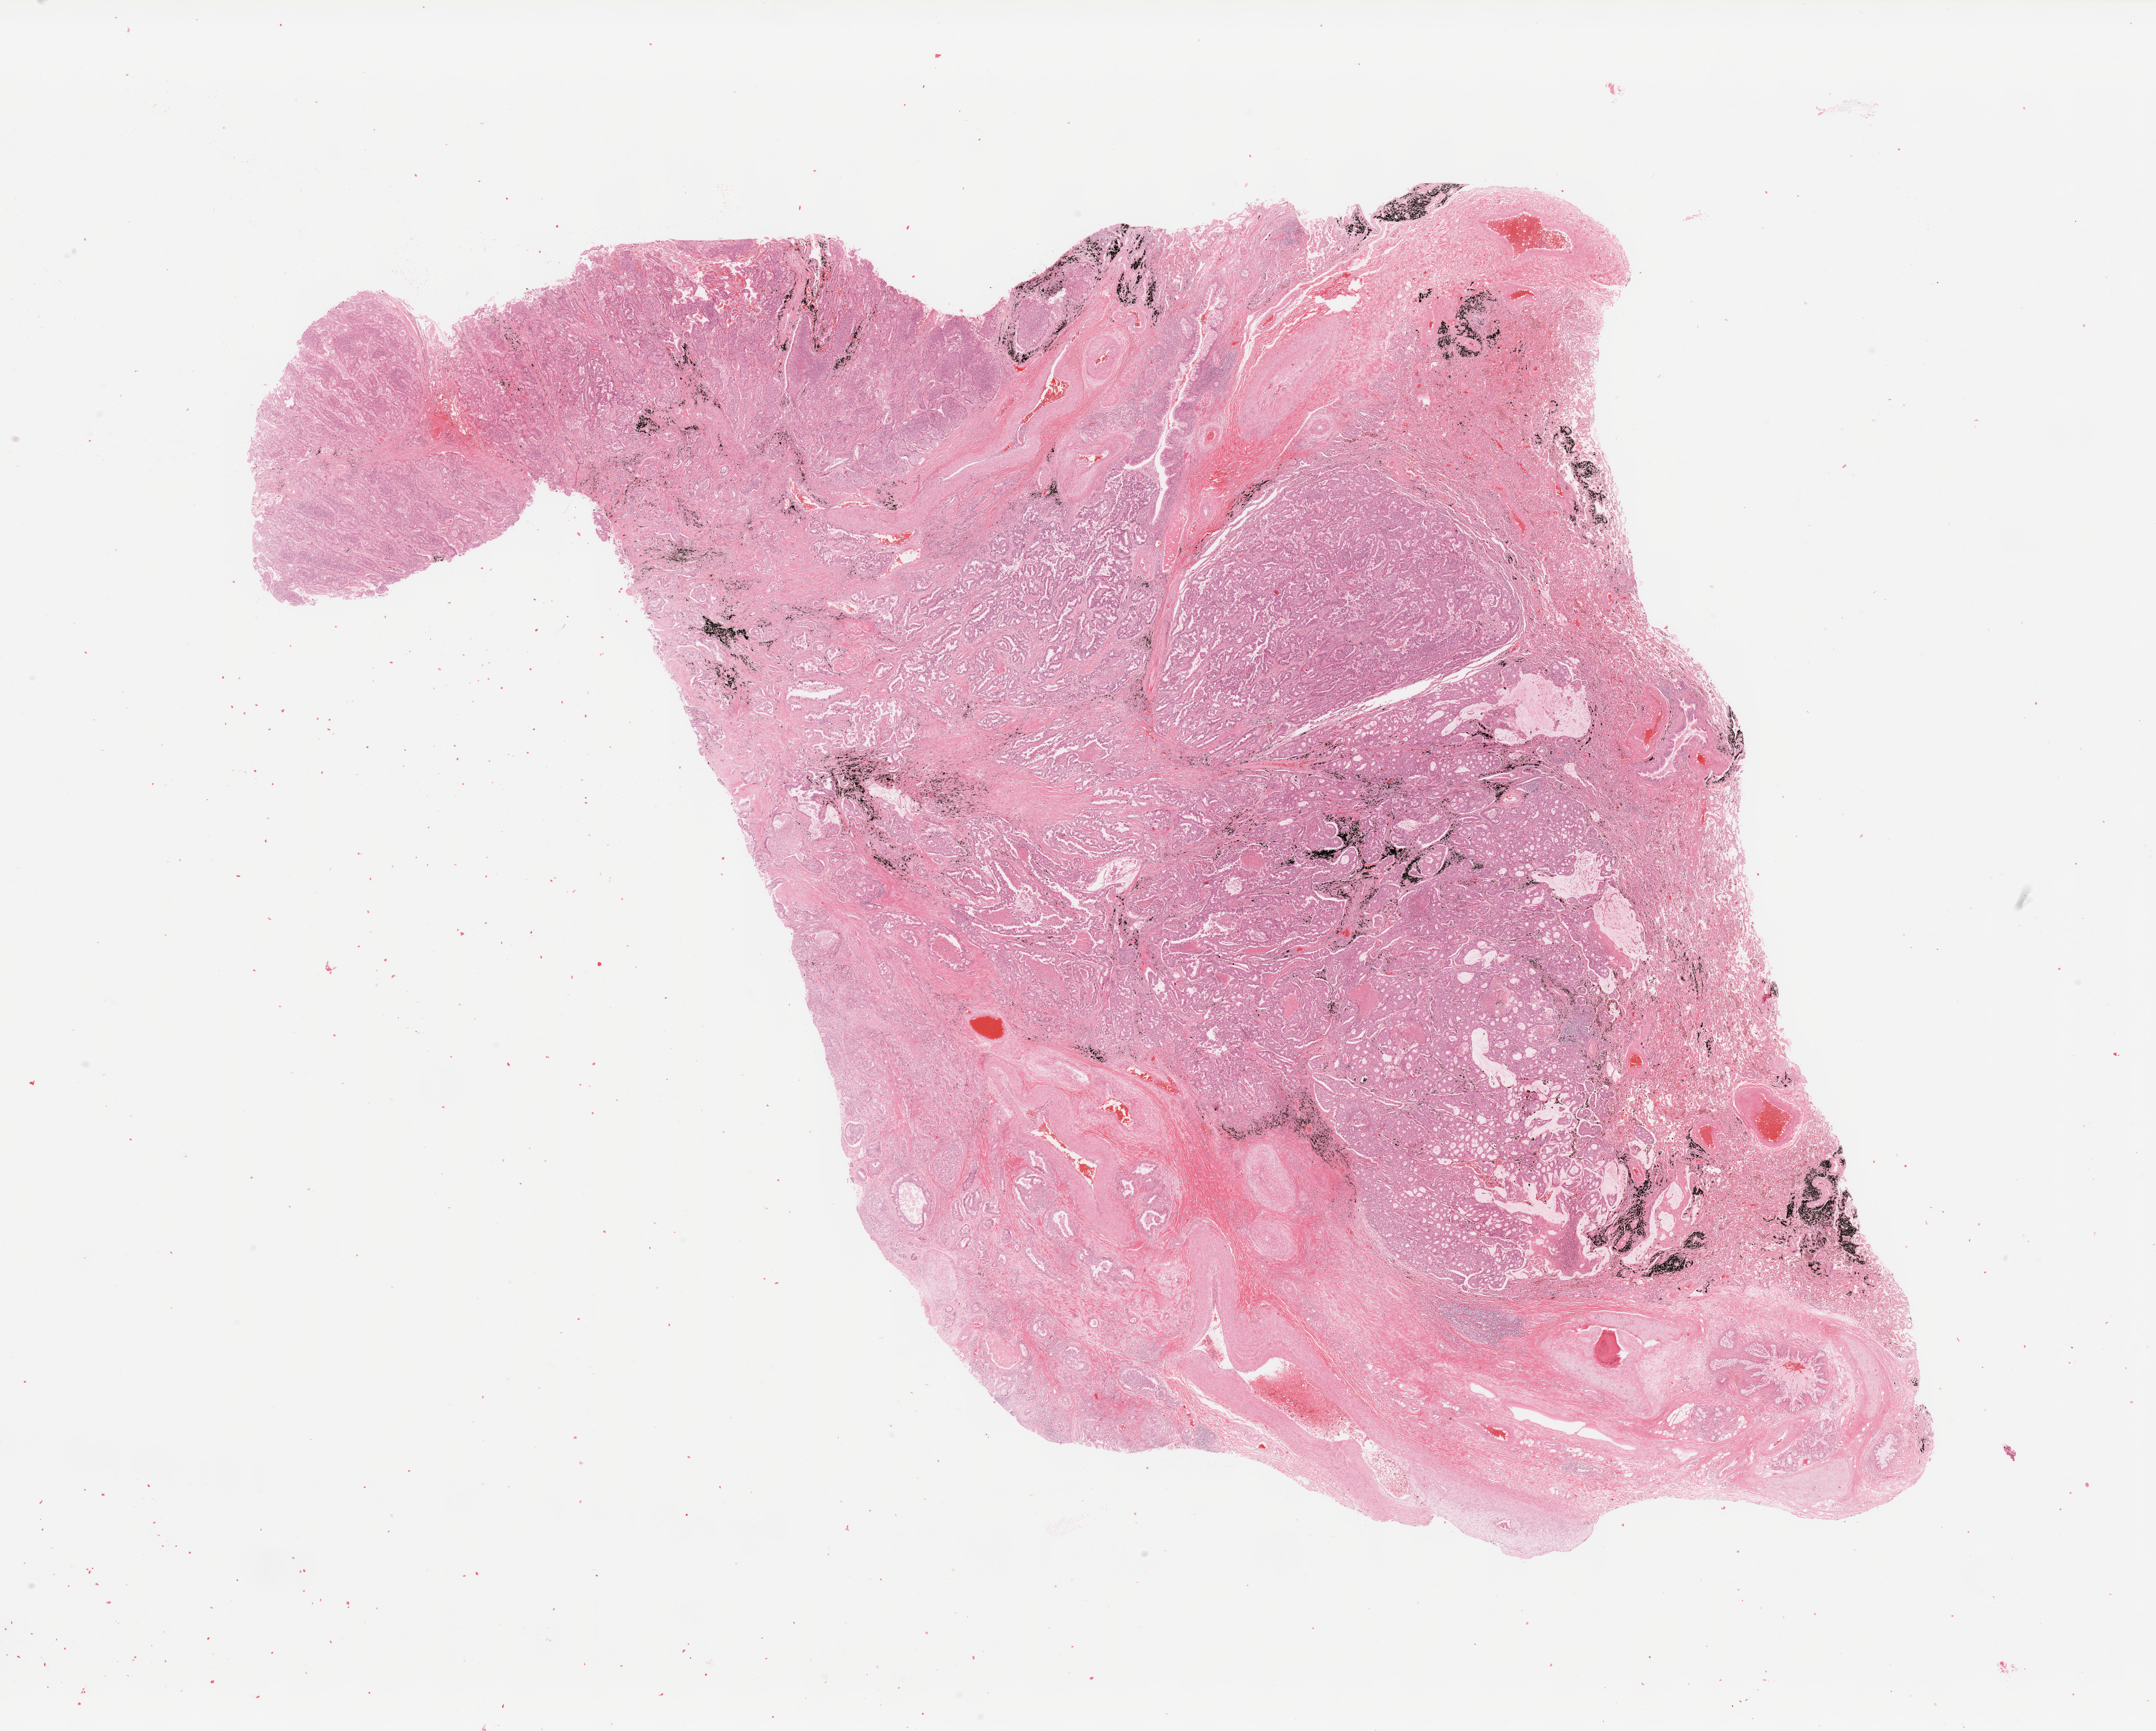
Digitized H&E tissue section (whole slide) — whole scanned area (about 28.5 x 22.9 mm) shown as a low-resolution overview; lung, tumour tissue. Patient: male, age 56 years. Histologic grade: G3 (poorly differentiated).
AJCC pathologic stage: IIIA. Diagnosis: Adenocarcinoma, NOS.